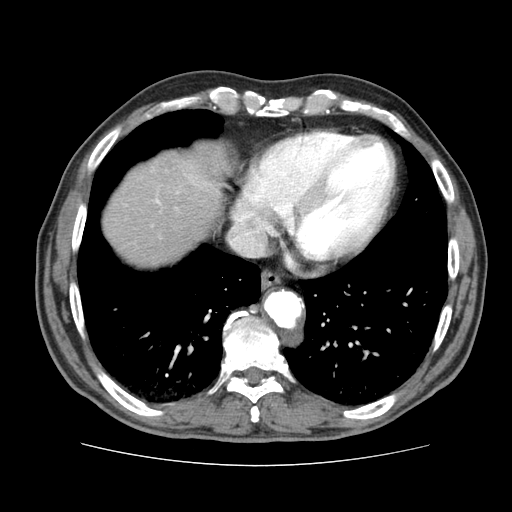
Contrast-enhanced abdominal CT (liver protocol), one axial slice. Position 72 of 79 along the scan axis. Reconstruction kernel STANDARD. 120 kVp. Soft-tissue window (W 400 / L 40 HU). 512 × 512 image matrix, field of view 360 × 360 mm. Case-level facts recorded for this patient, not image findings: diagnosis: hepatocellular carcinoma (patient treated with transarterial chemoembolisation; whether this scan precedes or follows treatment is not stated here); TNM stage (as recorded): Stage-I; Child-Pugh class: A.
Annotated regions visible in this slice (semi-automatically segmented with operator editing):
- abdominal aorta: bounding box <266,293,302,327> (left, top, right, bottom; pixels)
- liver parenchyma outside the tumour (the mass and vessels are separate outlines, so this box may not span the whole liver): <102,152,222,265>
- mass: <165,142,232,197>
- liver vessels: <156,200,160,203>